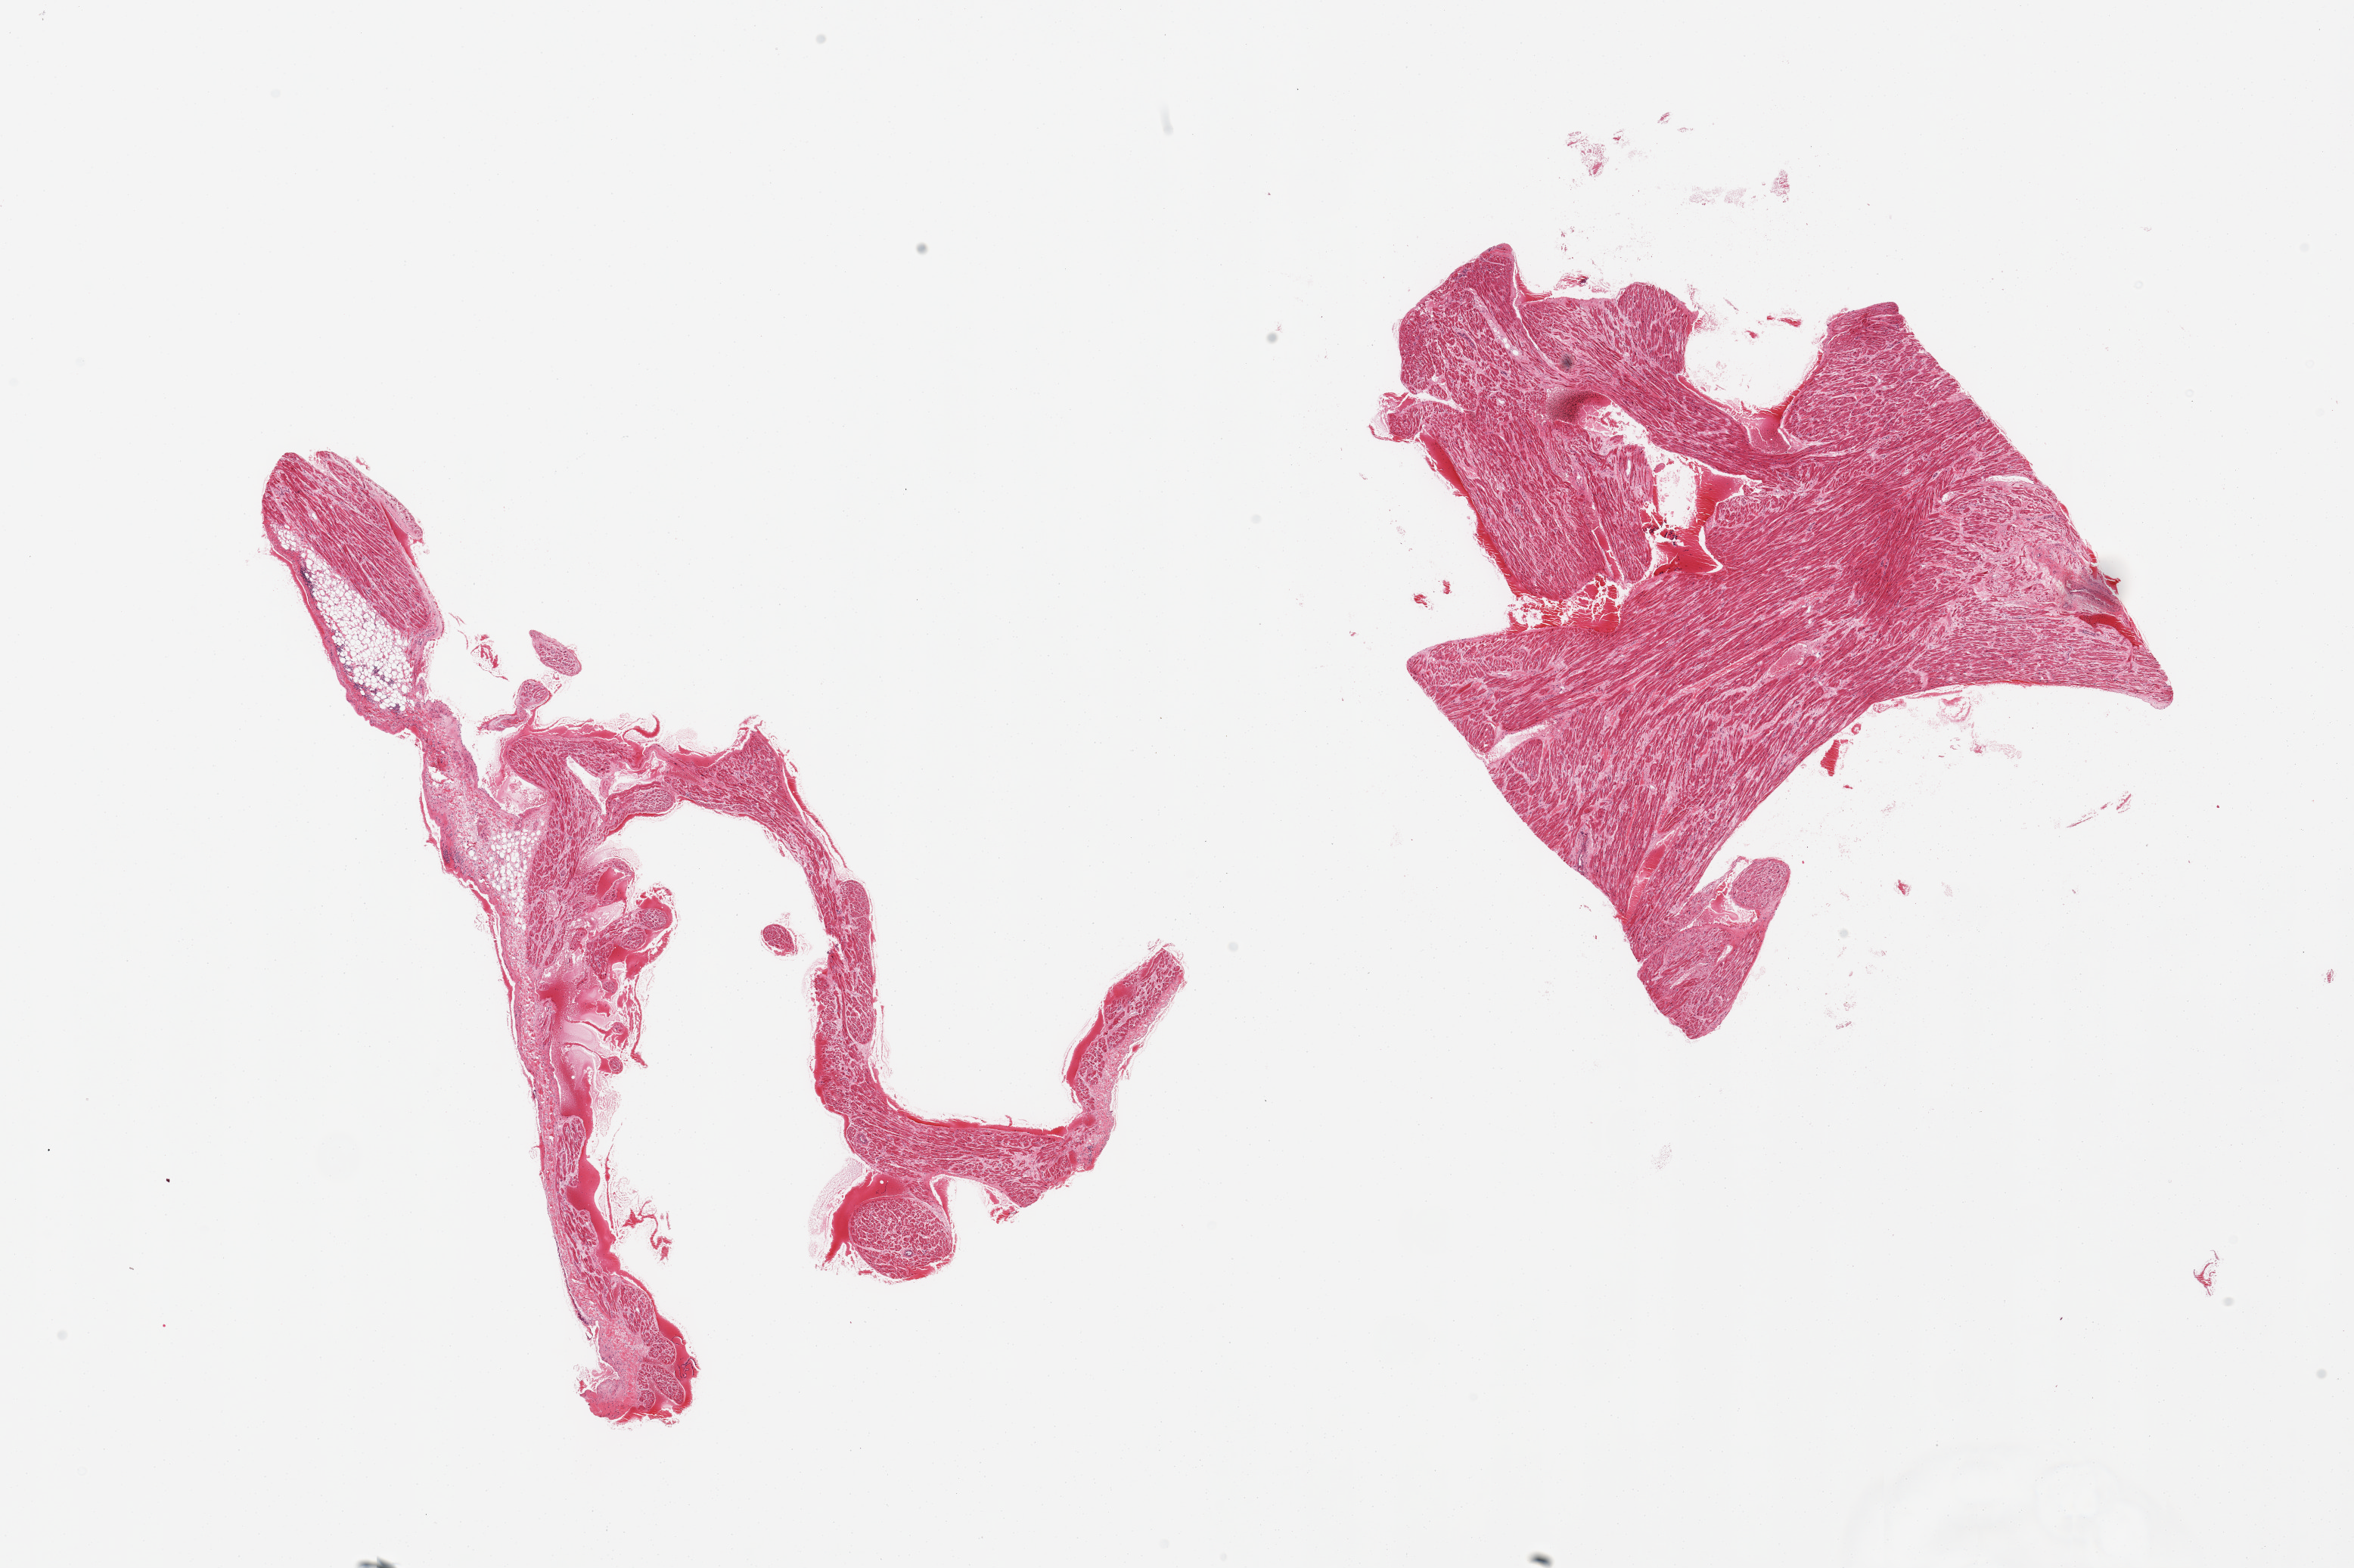
Digitized H&E-stained section, brightfield — low-resolution overview of the scanned area, about 24.6 x 16.4 mm. PAXgene-fixed paraffin-embedded (PFPE) section. Target tissue: auricular appendage. Donor tissue sample. Male donor.
Pathologist's review note for this sample: 2 pieces; 1 is all muscle; 1 50% fibrofatty.